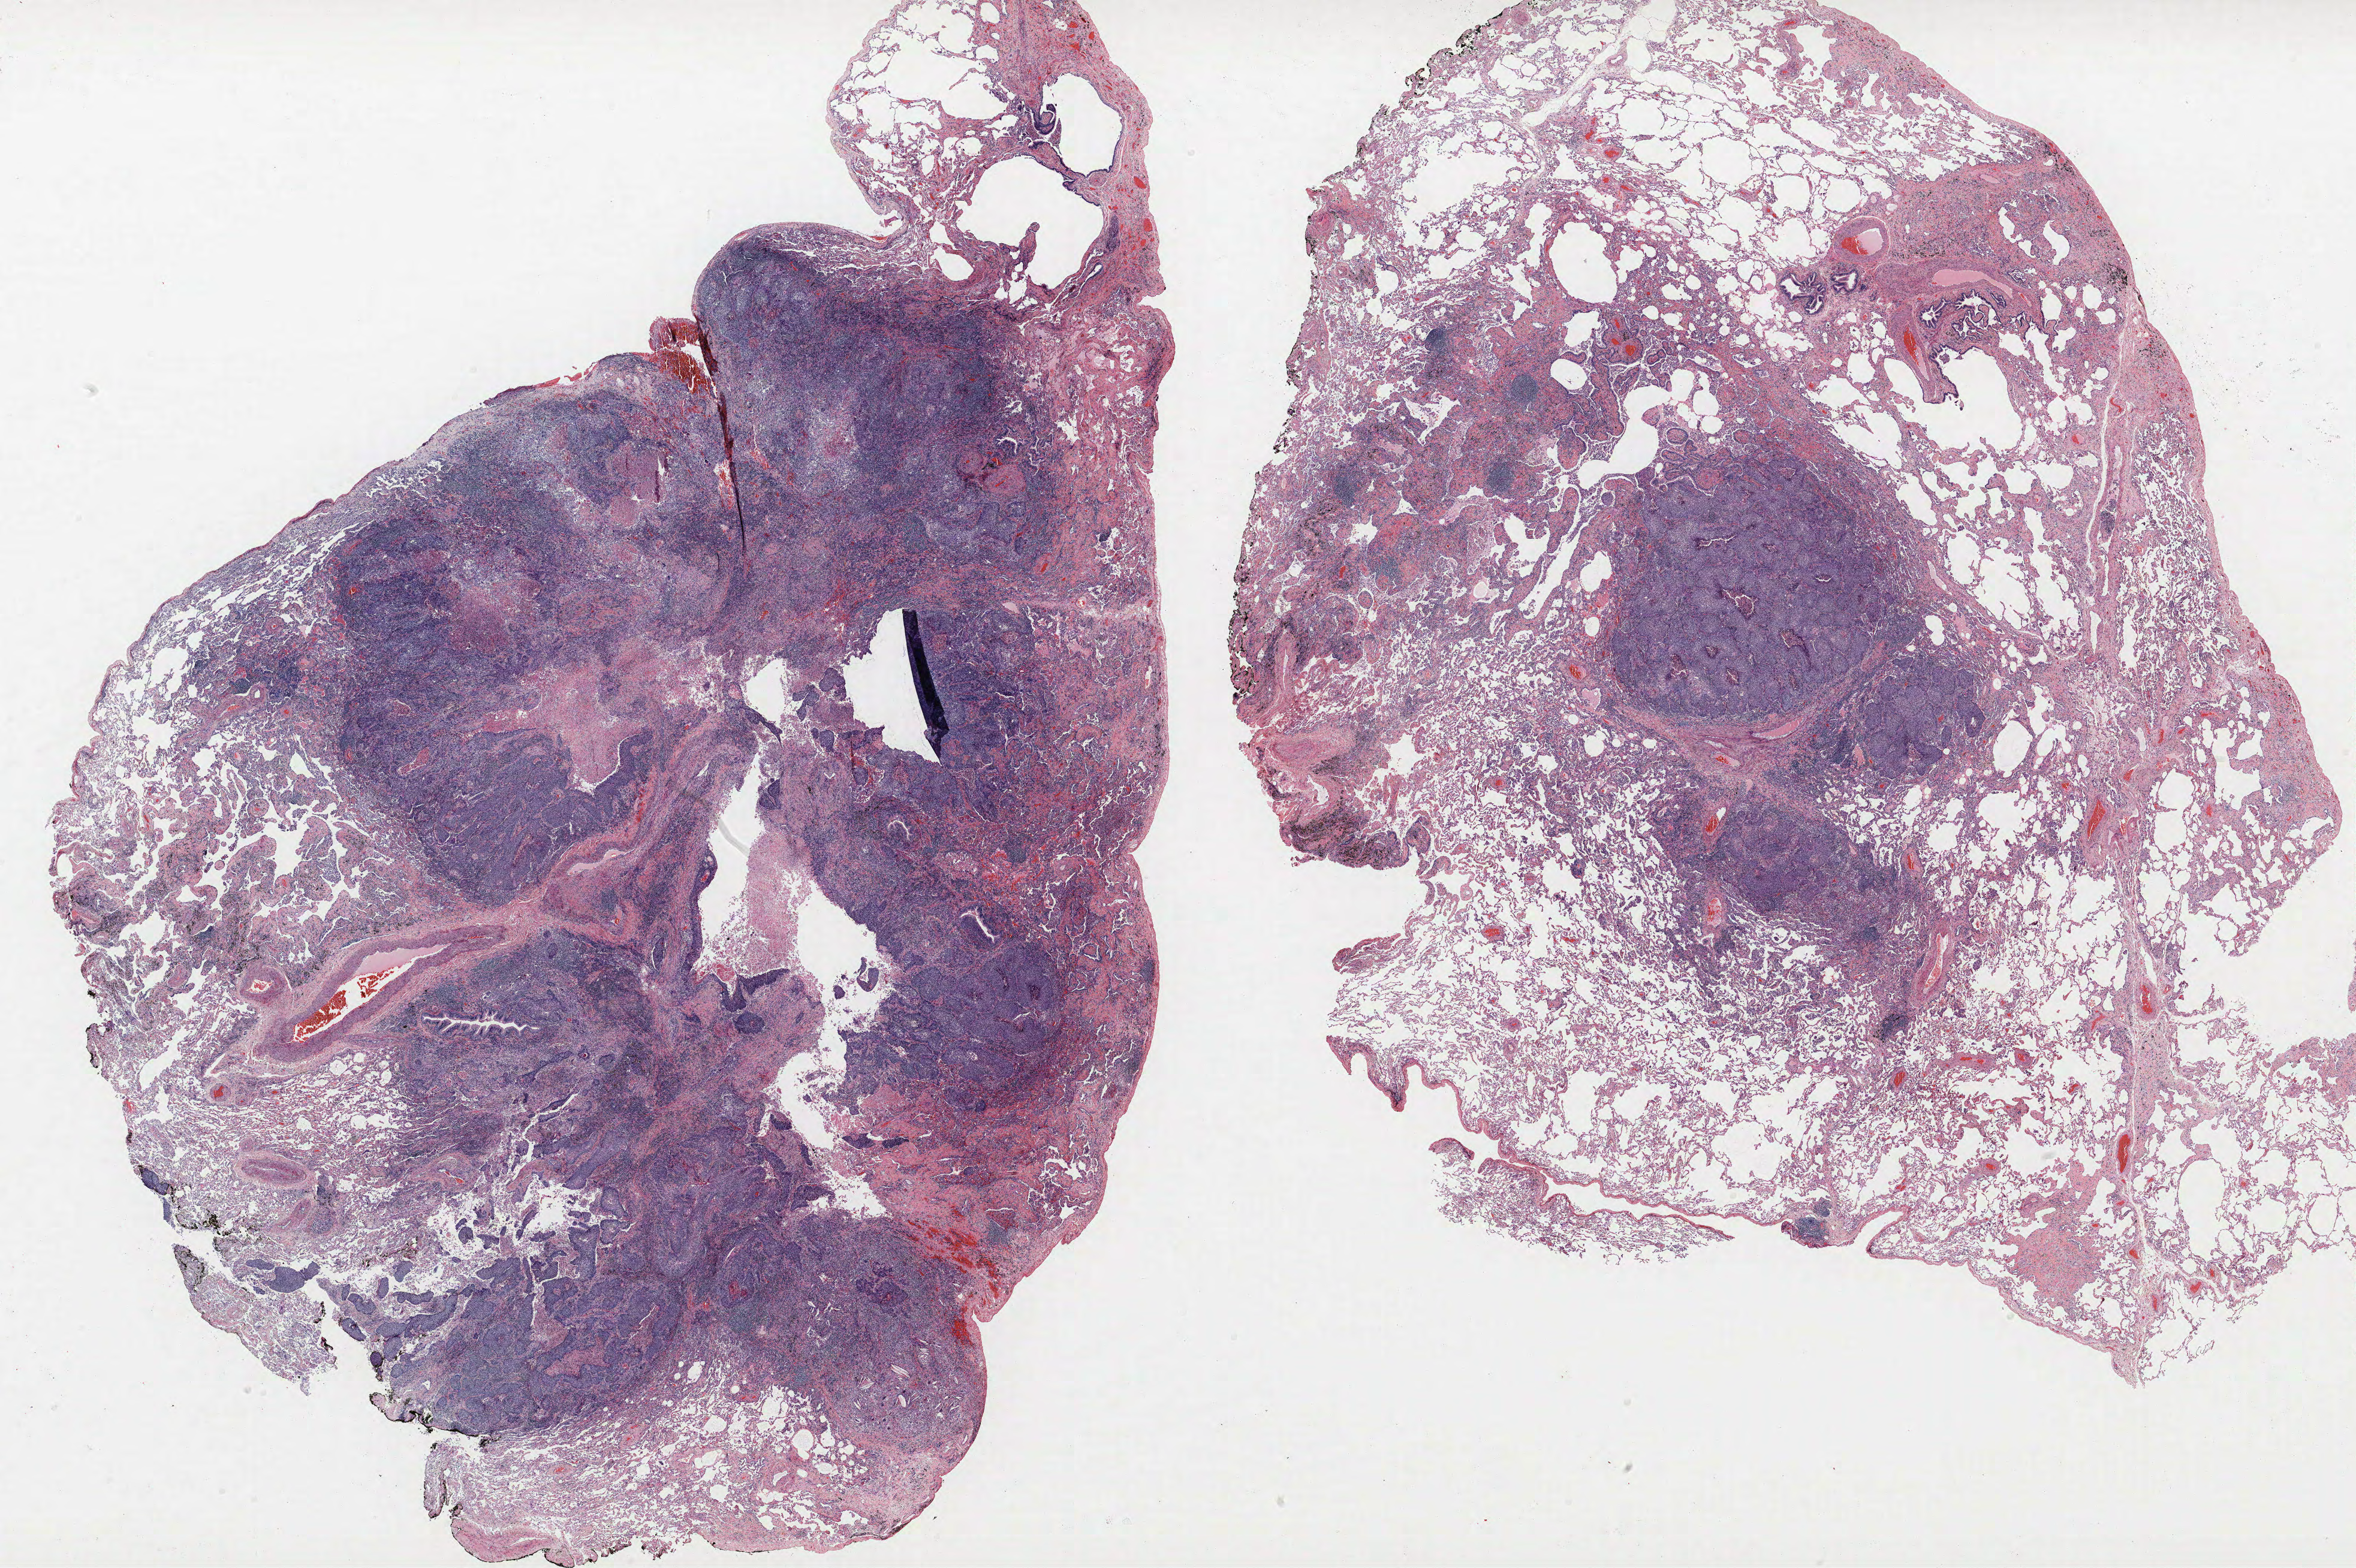
Whole-slide histology image, H&E-stained — shown as a low-resolution overview of the whole scanned area (about 31.4 x 20.9 mm, from a 40x scan), formalin-fixed paraffin-embedded (FFPE) section, lung tissue. Male patient, aged 69 at enrolment. Current smoker at enrolment.
Participant's lung-cancer diagnosis: Squamous cell carcinoma, NOS (ICD-O-3 8070/3).